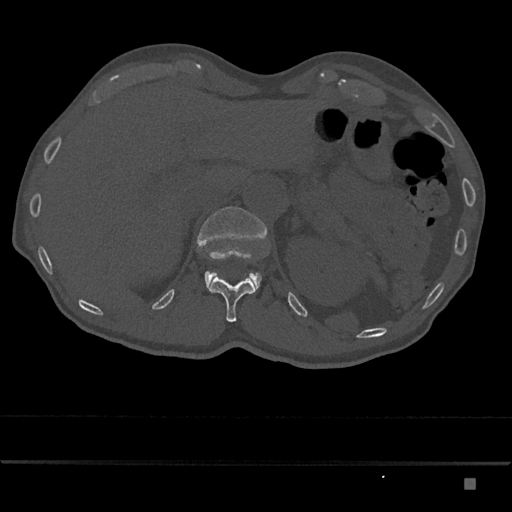
CT including the spine, one axial slice. Position 587 of 797 along the scan axis. 120 kVp. Bone window (W 1800 / L 400 HU). 512 × 512 image matrix, field of view 390 × 390 mm. Male patient, age 72 years. From the clinical record (not read from this slice): primary cancer: prostate.
Outlined on this slice (semi-automatically segmented with operator editing):
- L1 vertebra: bounding box (x1, y1, x2, y2) in pixels: (197, 207, 267, 291)
- T12 vertebra: (208, 276, 255, 322)